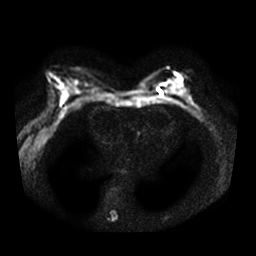
Breast MRI, one axial slice; position 18 of 38 along the scan axis; diffusion-weighted series; image 2 of 4 stored at this slice position (different b-values; order by instance number); 3 T; 5 mm slice thickness; 256 × 256 image matrix, field of view 340 × 340 mm. Female patient.
Structures marked on this image (outlined manually by an expert reader):
- tumour on diffusion-weighted imaging: bounding box <170,84,182,94> (left, top, right, bottom; pixels)